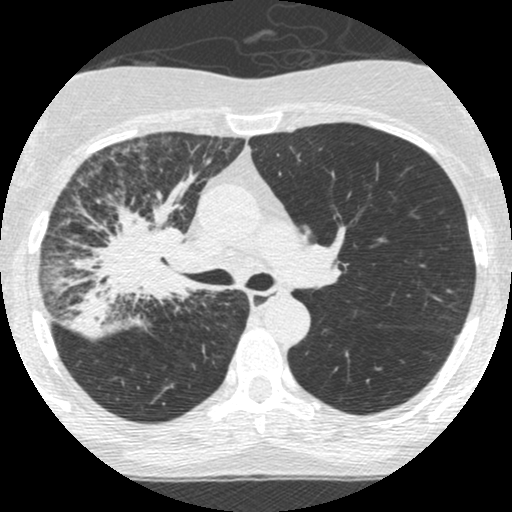
Low-dose screening chest CT, one axial slice; slice 166 of 253 in the series (ordered by position); 120 kVp; lung window (W 1500 / L -600 HU); 1.25 mm slice thickness; 512 × 512 image matrix, field of view 294 × 294 mm.
Outlined on this slice (expert manual segmentation):
- lesion 2 (tumor, hilum of right lung): box from (x=54, y=166) to (x=201, y=329) px